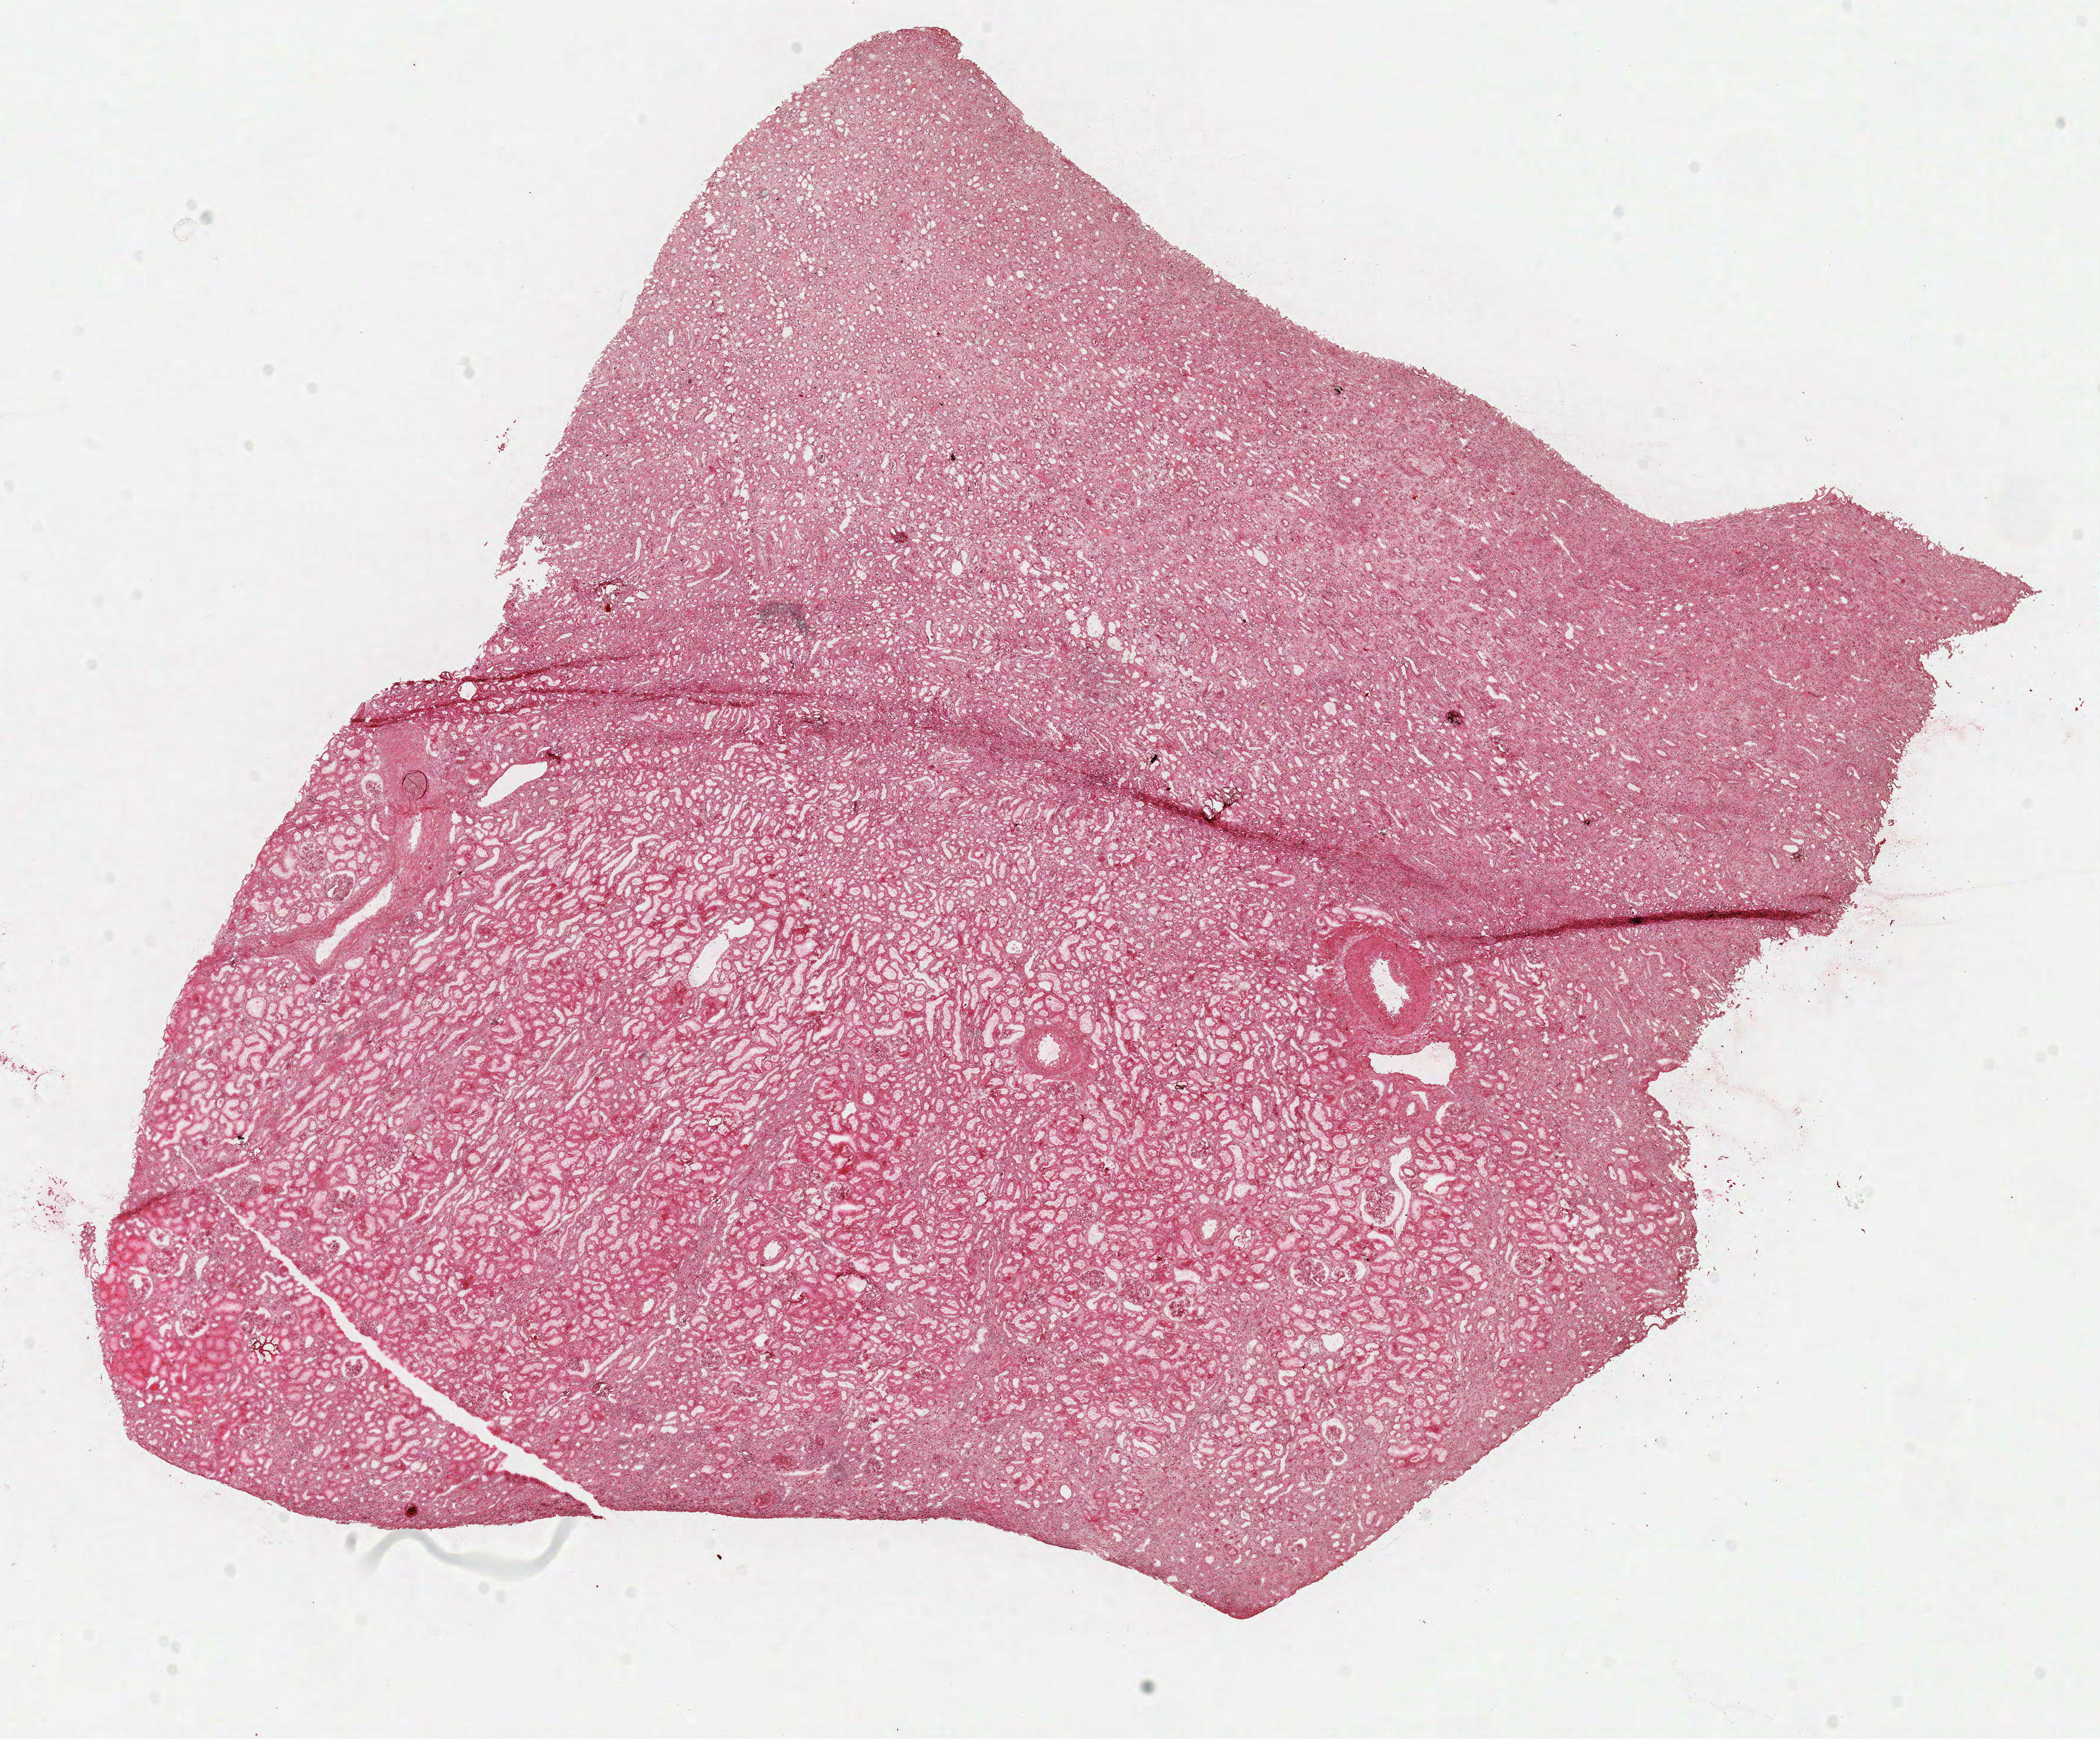
Whole-slide histology image, H&E-stained — whole scanned area (about 13.8 x 11.5 mm, acquisition: 40x scan) shown as a low-resolution overview; frozen section; solid tissue normal (non-tumour tissue) sample from the kidney. Patient: female, age at initial diagnosis 66 years.
This section: solid tissue normal sample (biorepository sample class). Patient diagnosis: Papillary adenocarcinoma, NOS.